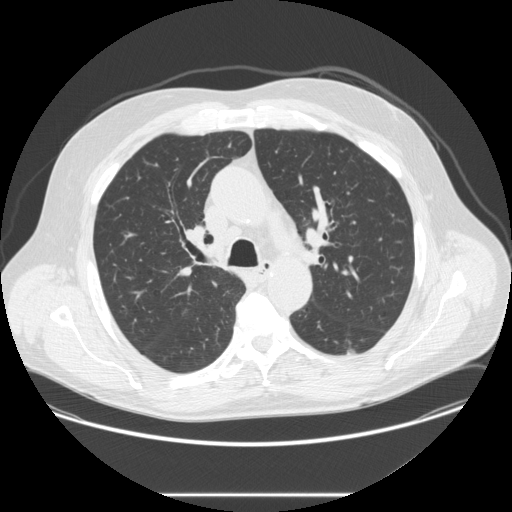
Low-dose screening chest CT, one axial slice. Slice 176 of 262 in the series (ordered by position). Lung window (W 1500 / L -600 HU). 2.5 mm slice thickness. 512 × 512 image matrix.
Annotated regions visible in this slice (expert manual segmentation):
- lesion 1 (tumor, lower lobe of left lung): bounding box <347,349,355,354> (left, top, right, bottom; pixels)